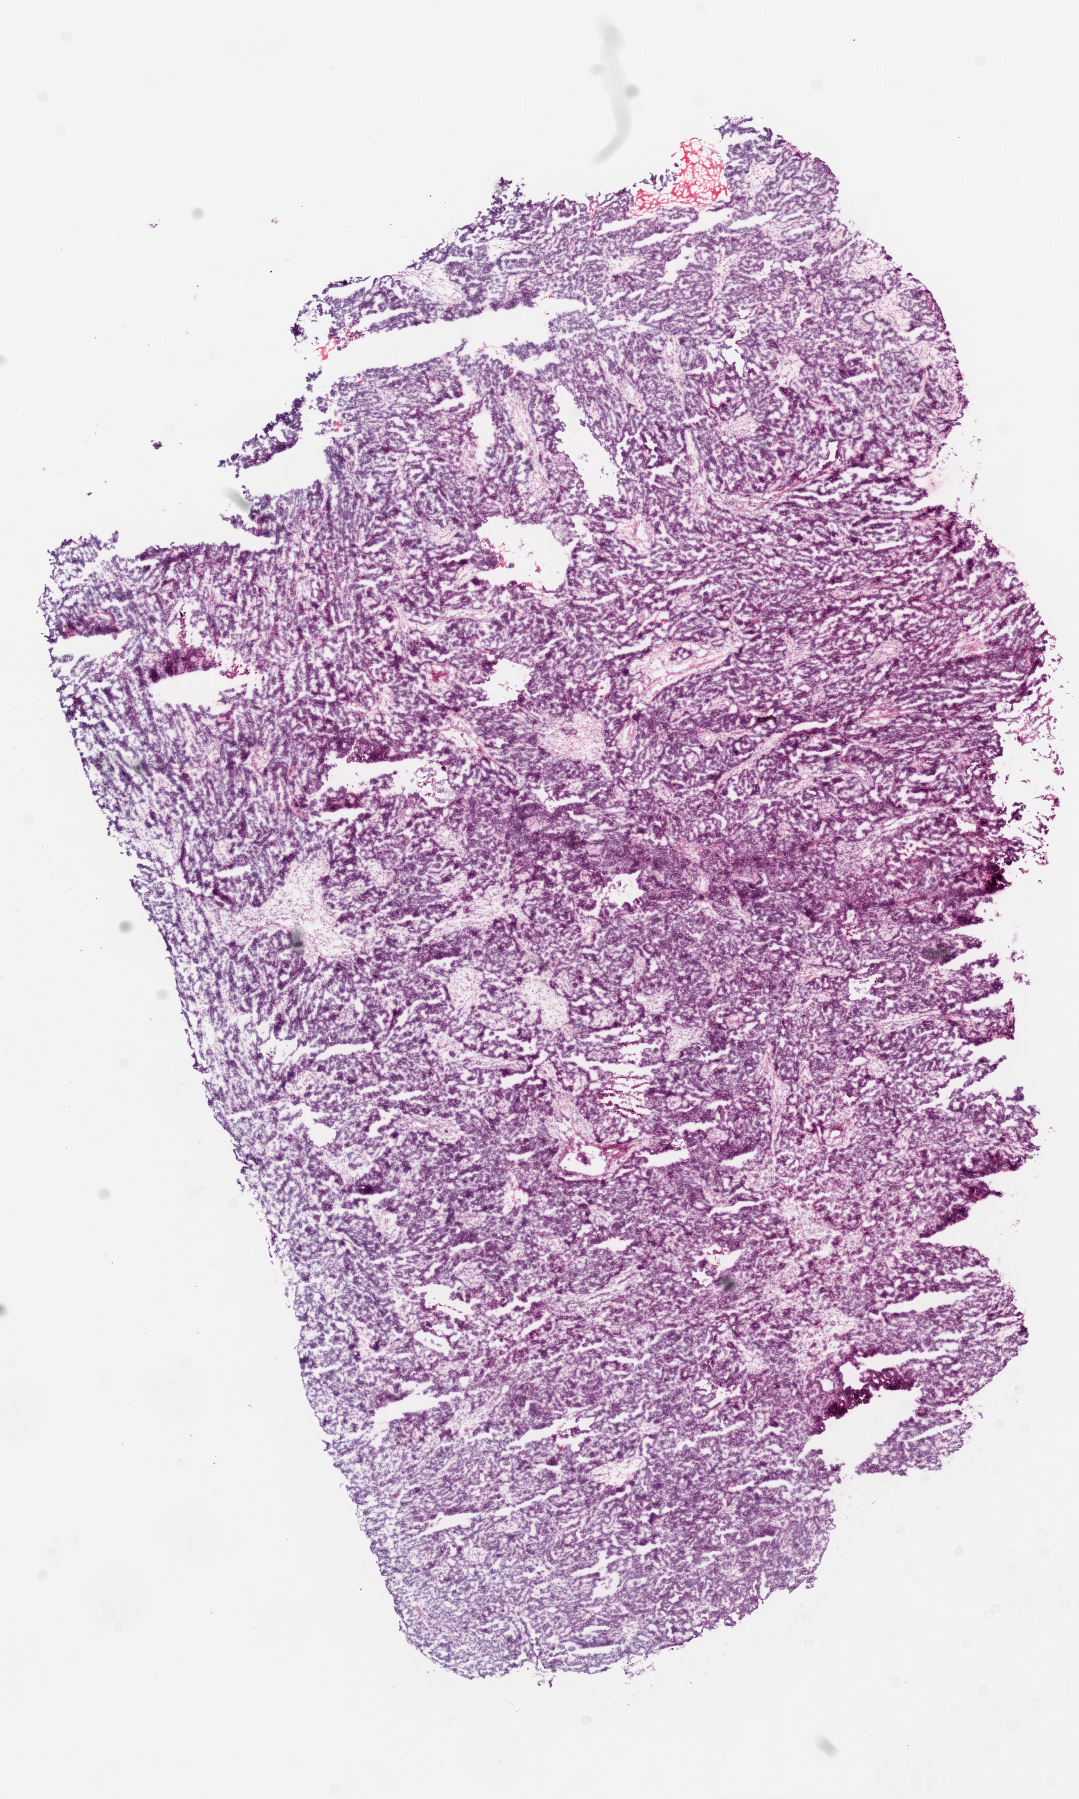
Whole-slide histology image, H&E-stained — low-resolution overview of the scanned area, about 8.7 x 14.5 mm; frozen section from the top of the tissue portion; sample: primary tumour, ovary. Female patient; age at initial diagnosis 65 years. Histologic grade: G3 (poorly differentiated). Slide review estimates, as recorded: tumour cells 90%, tumour nuclei 95%, normal cells 0%, stromal cells 10%, necrosis 0%.
FIGO stage: IIIC. Histologic diagnosis: Serous cystadenocarcinoma, NOS.